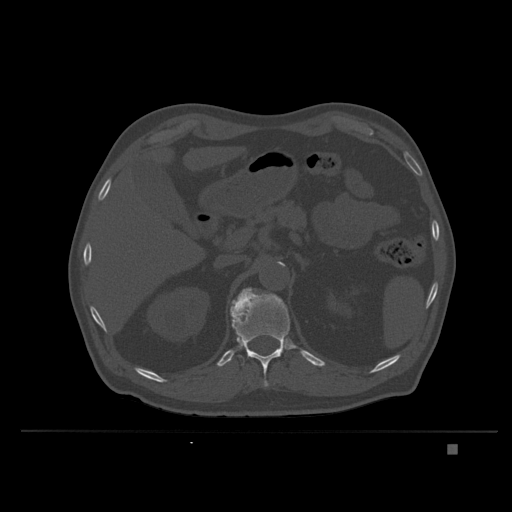
CT including the spine, one axial slice; position 157 of 435 along the scan axis; bone window (W 1800 / L 400 HU); 1.5 mm slice thickness; 512 × 512 image matrix. Male patient, age 73 years. From the clinical record (not read from this slice): primary cancer: skin.
Structures marked on this image (semi-automatically segmented with operator editing):
- T12 vertebra: bounding box <230,292,290,387> (left, top, right, bottom; pixels)